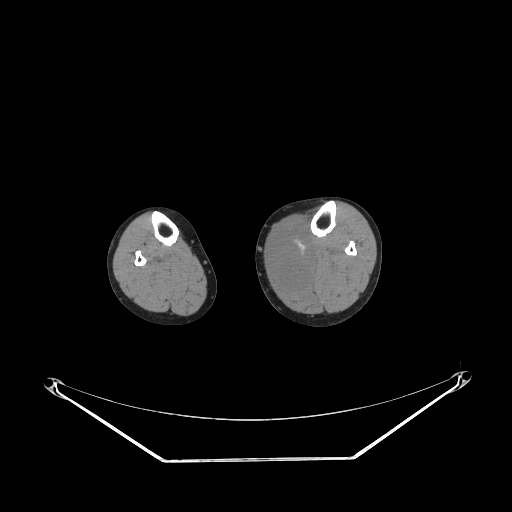
CT of an extremity soft-tissue mass (from a PET/CT study), one axial slice; position 136 of 223 along the scan axis; reconstruction kernel STANDARD; 140 kVp; soft-tissue window (W 400 / L 40 HU); 512 × 512 image matrix. Female patient. Case-level facts recorded for this patient, not image findings: histological type: extraskeletal high grade osteogenic sarcoma; grade: high; site of the primary tumour: left calf.
Annotated regions visible in this slice (expert contour drawn on MRI and transferred to this co-registered scan by the dataset authors):
- gross tumour volume (mass): bounding box (x1, y1, x2, y2) in pixels: (272, 230, 312, 286)